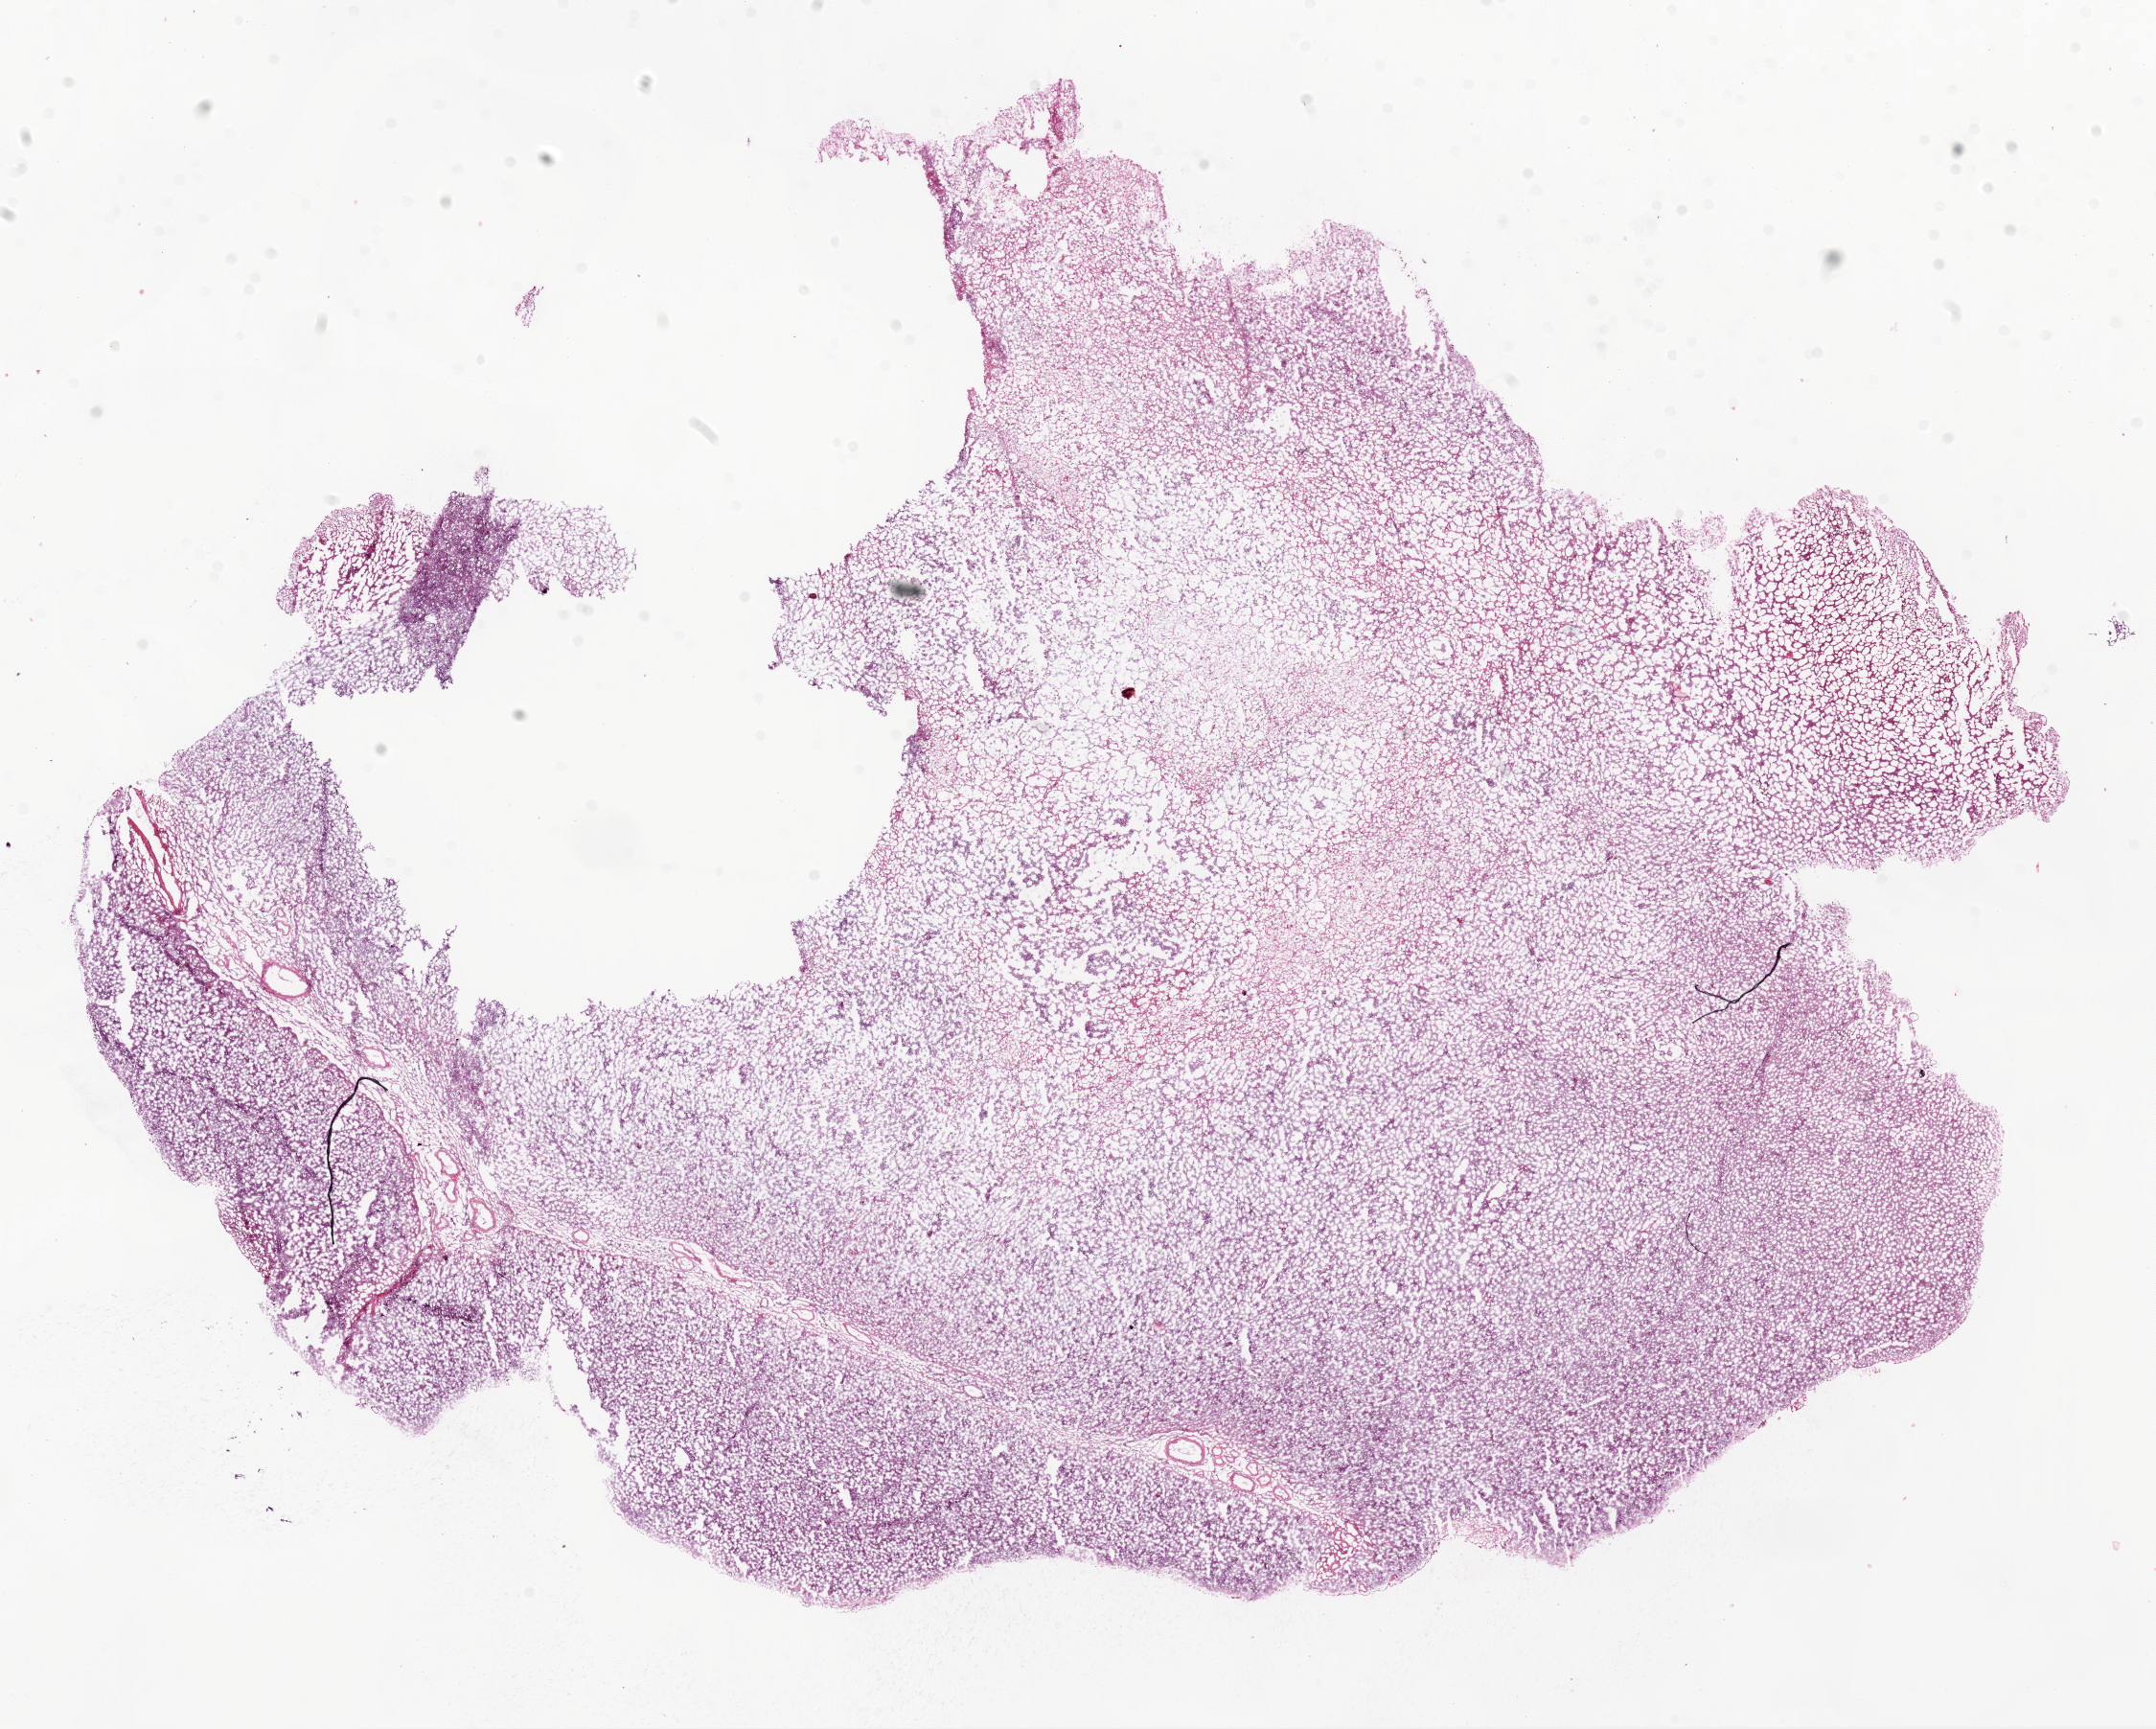
Digitized H&E-stained tissue section (whole slide), whole scanned area (about 18.1 x 14.5 mm, acquisition: 20x scan) shown as a low-resolution overview. Frozen section from the bottom of the tissue portion. Sample: primary tumour, brain. Male patient; age at initial diagnosis 57 years. Slide review estimates, as recorded: tumour cells 99%, tumour nuclei 80%, normal cells 0%, stromal cells 0%, necrosis 1%.
* pathologic diagnosis: Glioblastoma